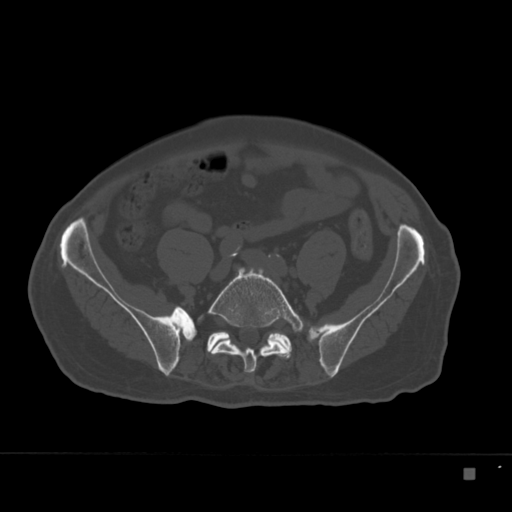
CT including the spine, one axial slice. Position 19 of 332 along the scan axis. Reconstruction kernel Br40s. 120 kVp. Bone window (W 1800 / L 400 HU). 1.5 mm slice thickness. 512 × 512 image matrix, field of view 389 × 389 mm. Male patient, age 72 years. From the clinical record (not read from this slice): primary cancer: skeletal.
Structures marked on this image (semi-automatically segmented with operator editing):
- L5 vertebra: bounding box (x1, y1, x2, y2) in pixels: (198, 267, 304, 373)